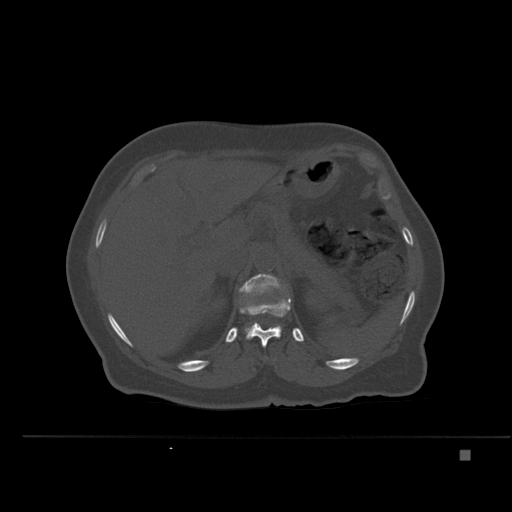
CT including the spine, one axial slice. Slice 250 of 477 in the series (ordered by position). Bone window (W 1800 / L 400 HU). 512 × 512 image matrix. Patient: female, 74 years. Case-level facts recorded for this patient, not image findings: primary cancer: colon.
Annotated regions visible in this slice (semi-automatic segmentation, software-assisted and operator-edited):
- L1 vertebra: bounding box (x1, y1, x2, y2) in pixels: (239, 273, 281, 333)
- T12 vertebra: (240, 298, 291, 347)